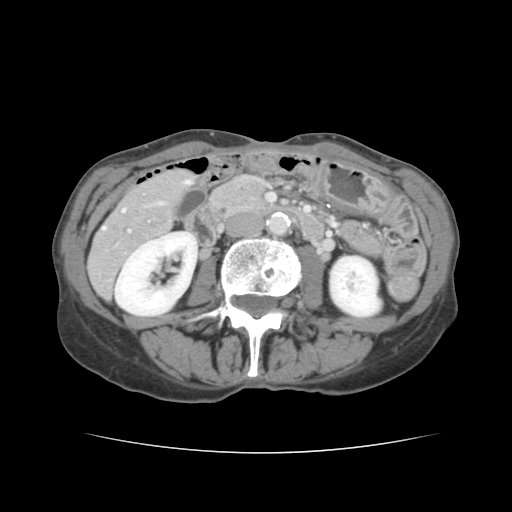
Contrast-enhanced abdominal CT, one axial slice. Position 42 of 136 along the scan axis. 120 kVp. Intravenous contrast given. Soft-tissue window (W 400 / L 40 HU). 2.5 mm slice thickness. 512 × 512 image matrix, field of view 319 × 319 mm. Female patient, age 77 years. Case-level facts recorded for this patient, not image findings: diagnosis: colorectal cancer liver metastases, imaged before liver resection; multiple liver metastases: yes; largest metastasis: 3 cm; disease in both lobes: no.
Structures marked on this image (expert manual segmentation):
- hepatic veins: bounding box [x1, y1, x2, y2] px = [103, 181, 190, 230]
- liver: [89, 170, 190, 295]
- planned liver remnant (the part of the liver to remain after resection): [183, 175, 187, 178]
- portal vein (with intrahepatic branches): [128, 230, 131, 232]